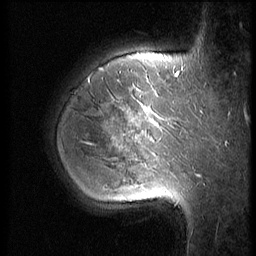
Breast MRI (dynamic contrast-enhanced), one sagittal slice. Slice 47 of 56 in the series (ordered by position). 3 images stored at this slice position (order not interpretable as contrast timing). 1.5 T. TE 4.2 ms, TR 9 ms. 2.5 mm slice thickness. 256 × 256 image matrix, field of view 180 × 180 mm. Patient: female, 35 years. Case-level facts recorded for this patient, not image findings: setting: breast cancer imaged before/during neoadjuvant chemotherapy; receptor status: HR-positive, HER2-negative.
Outlined on this slice (semi-automatically segmented with operator editing):
- analysis volume of interest (the breast-tissue region the enhancement analysis was run in; not a lesion): bounding box (x1, y1, x2, y2) in pixels: (63, 60, 190, 218)
- tumour enhancement mask (voxels above the 140 % enhancement threshold inside the analysis volume of interest): (141, 107, 158, 167)